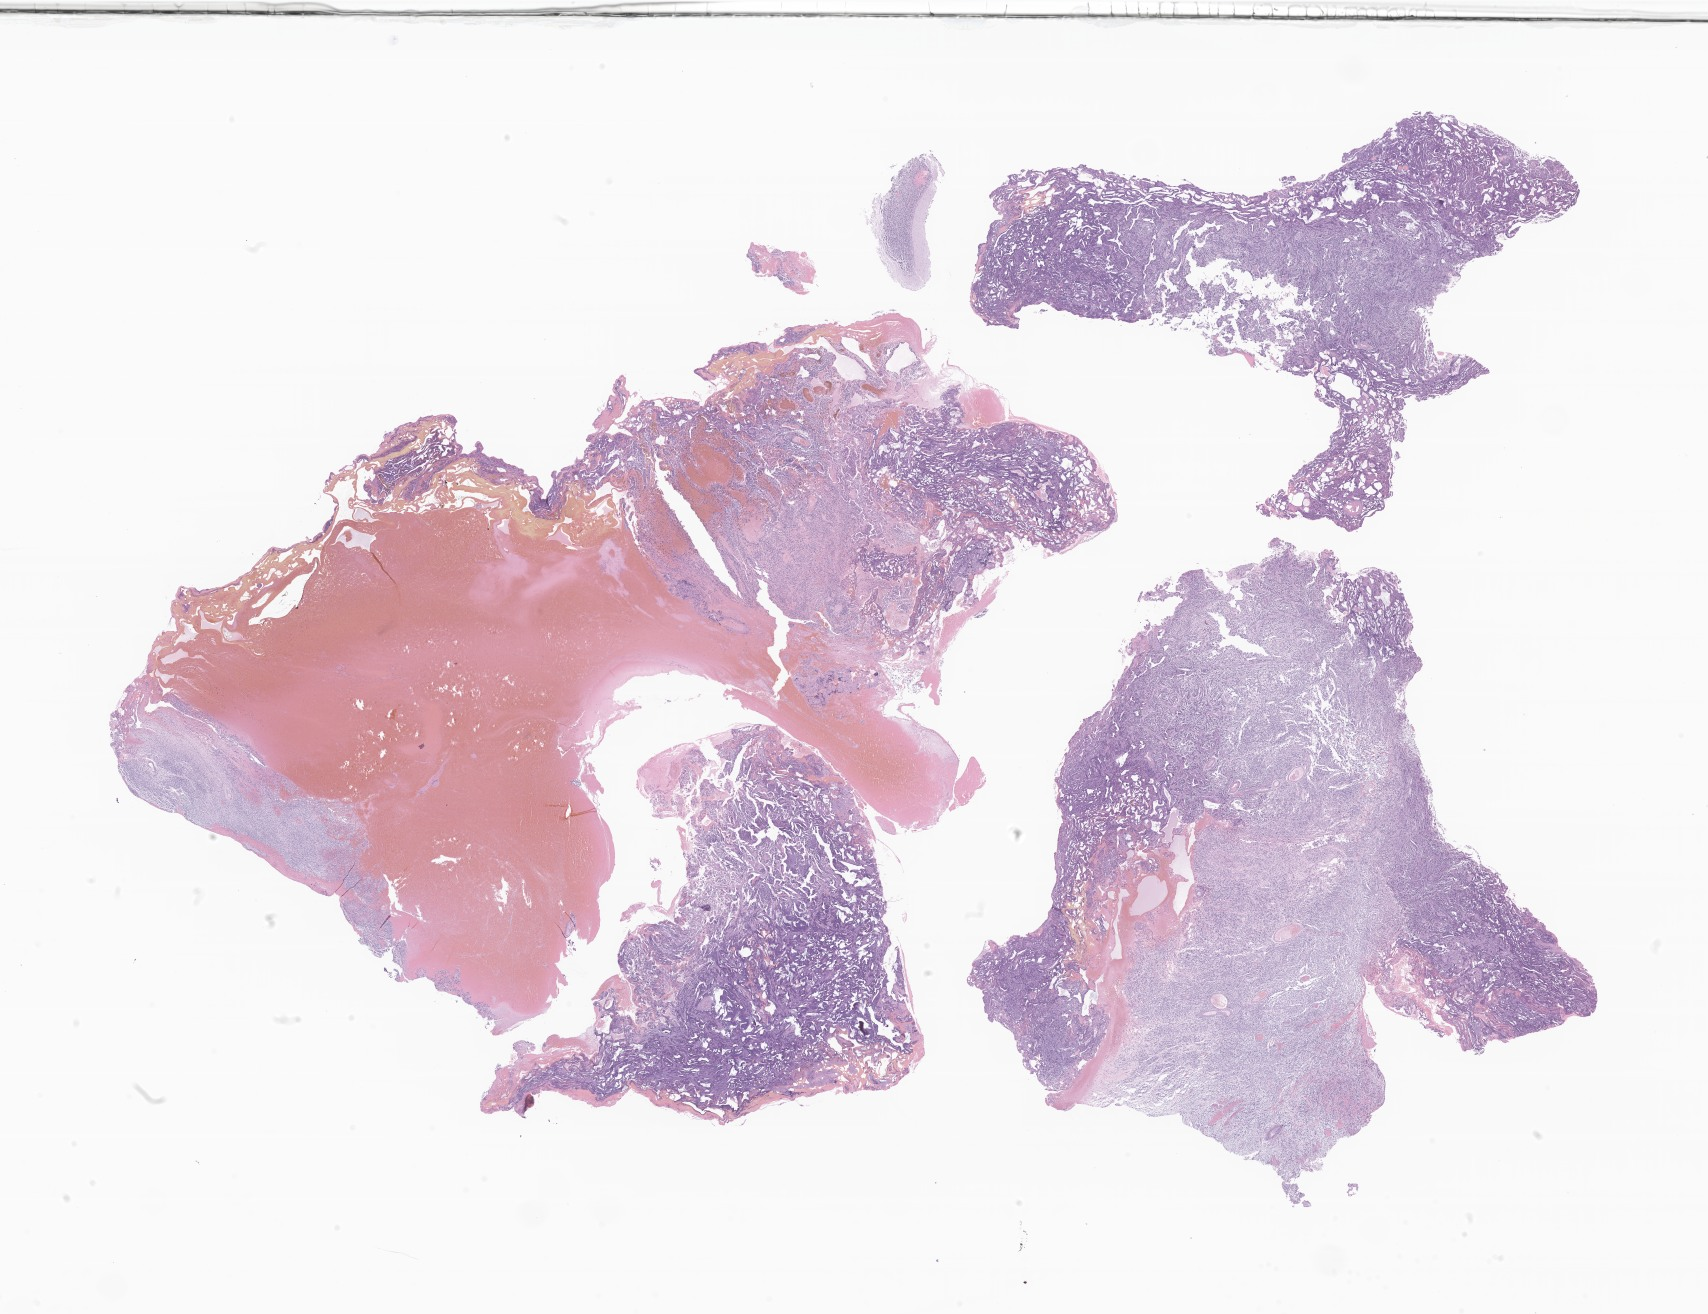
Haematoxylin and eosin whole-slide image of tumor tissue from the cerebellum — a low-resolution overview of the entire scanned area, about 28.8 x 22.2 mm. Formalin-fixed paraffin-embedded section. Patient: female, age 122 months (10 years 2 months).
Diagnosis: Medulloblastoma, NOS.